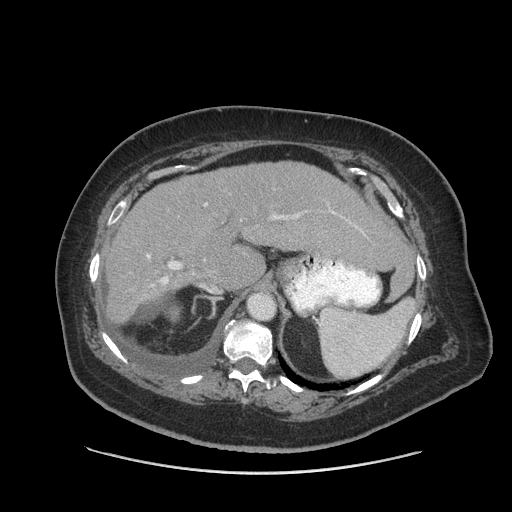
Contrast-enhanced abdominal CT (liver protocol), one axial slice; position 58 of 91 along the scan axis; reconstruction kernel STANDARD; 140 kVp; soft-tissue window (W 400 / L 40 HU); 512 × 512 image matrix, field of view 420 × 420 mm. Case-level facts recorded for this patient, not image findings: diagnosis: hepatocellular carcinoma (patient treated with transarterial chemoembolisation; whether this scan precedes or follows treatment is not stated here); TNM stage (as recorded): Stage-I; Child-Pugh class: A; tumour differentiation: well differentiated; tumour nodularity: uninodular.
Structures marked on this image (semi-automatic segmentation, software-assisted and operator-edited):
- liver parenchyma outside the tumour (the mass and vessels are separate outlines, so this box may not span the whole liver): bounding box <102,162,402,322> (left, top, right, bottom; pixels)
- liver vessels: <147,203,358,286>